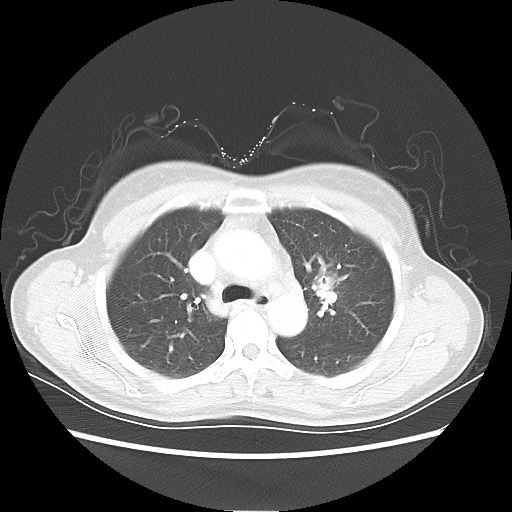
Chest CT, one axial slice; slice 38 of 54 in the series (ordered by position); lung window (W 1500 / L -600 HU); 512 × 512 image matrix. Patient: female, 53 years. Case-level facts recorded for this patient, not image findings: clinical TNM (as recorded): T1c N0 M0.
Outlined on this slice (rectangle marked by the reading radiologist):
- lung tumour (recorded histology: adenocarcinoma): bounding box <309,265,351,313> (left, top, right, bottom; pixels)